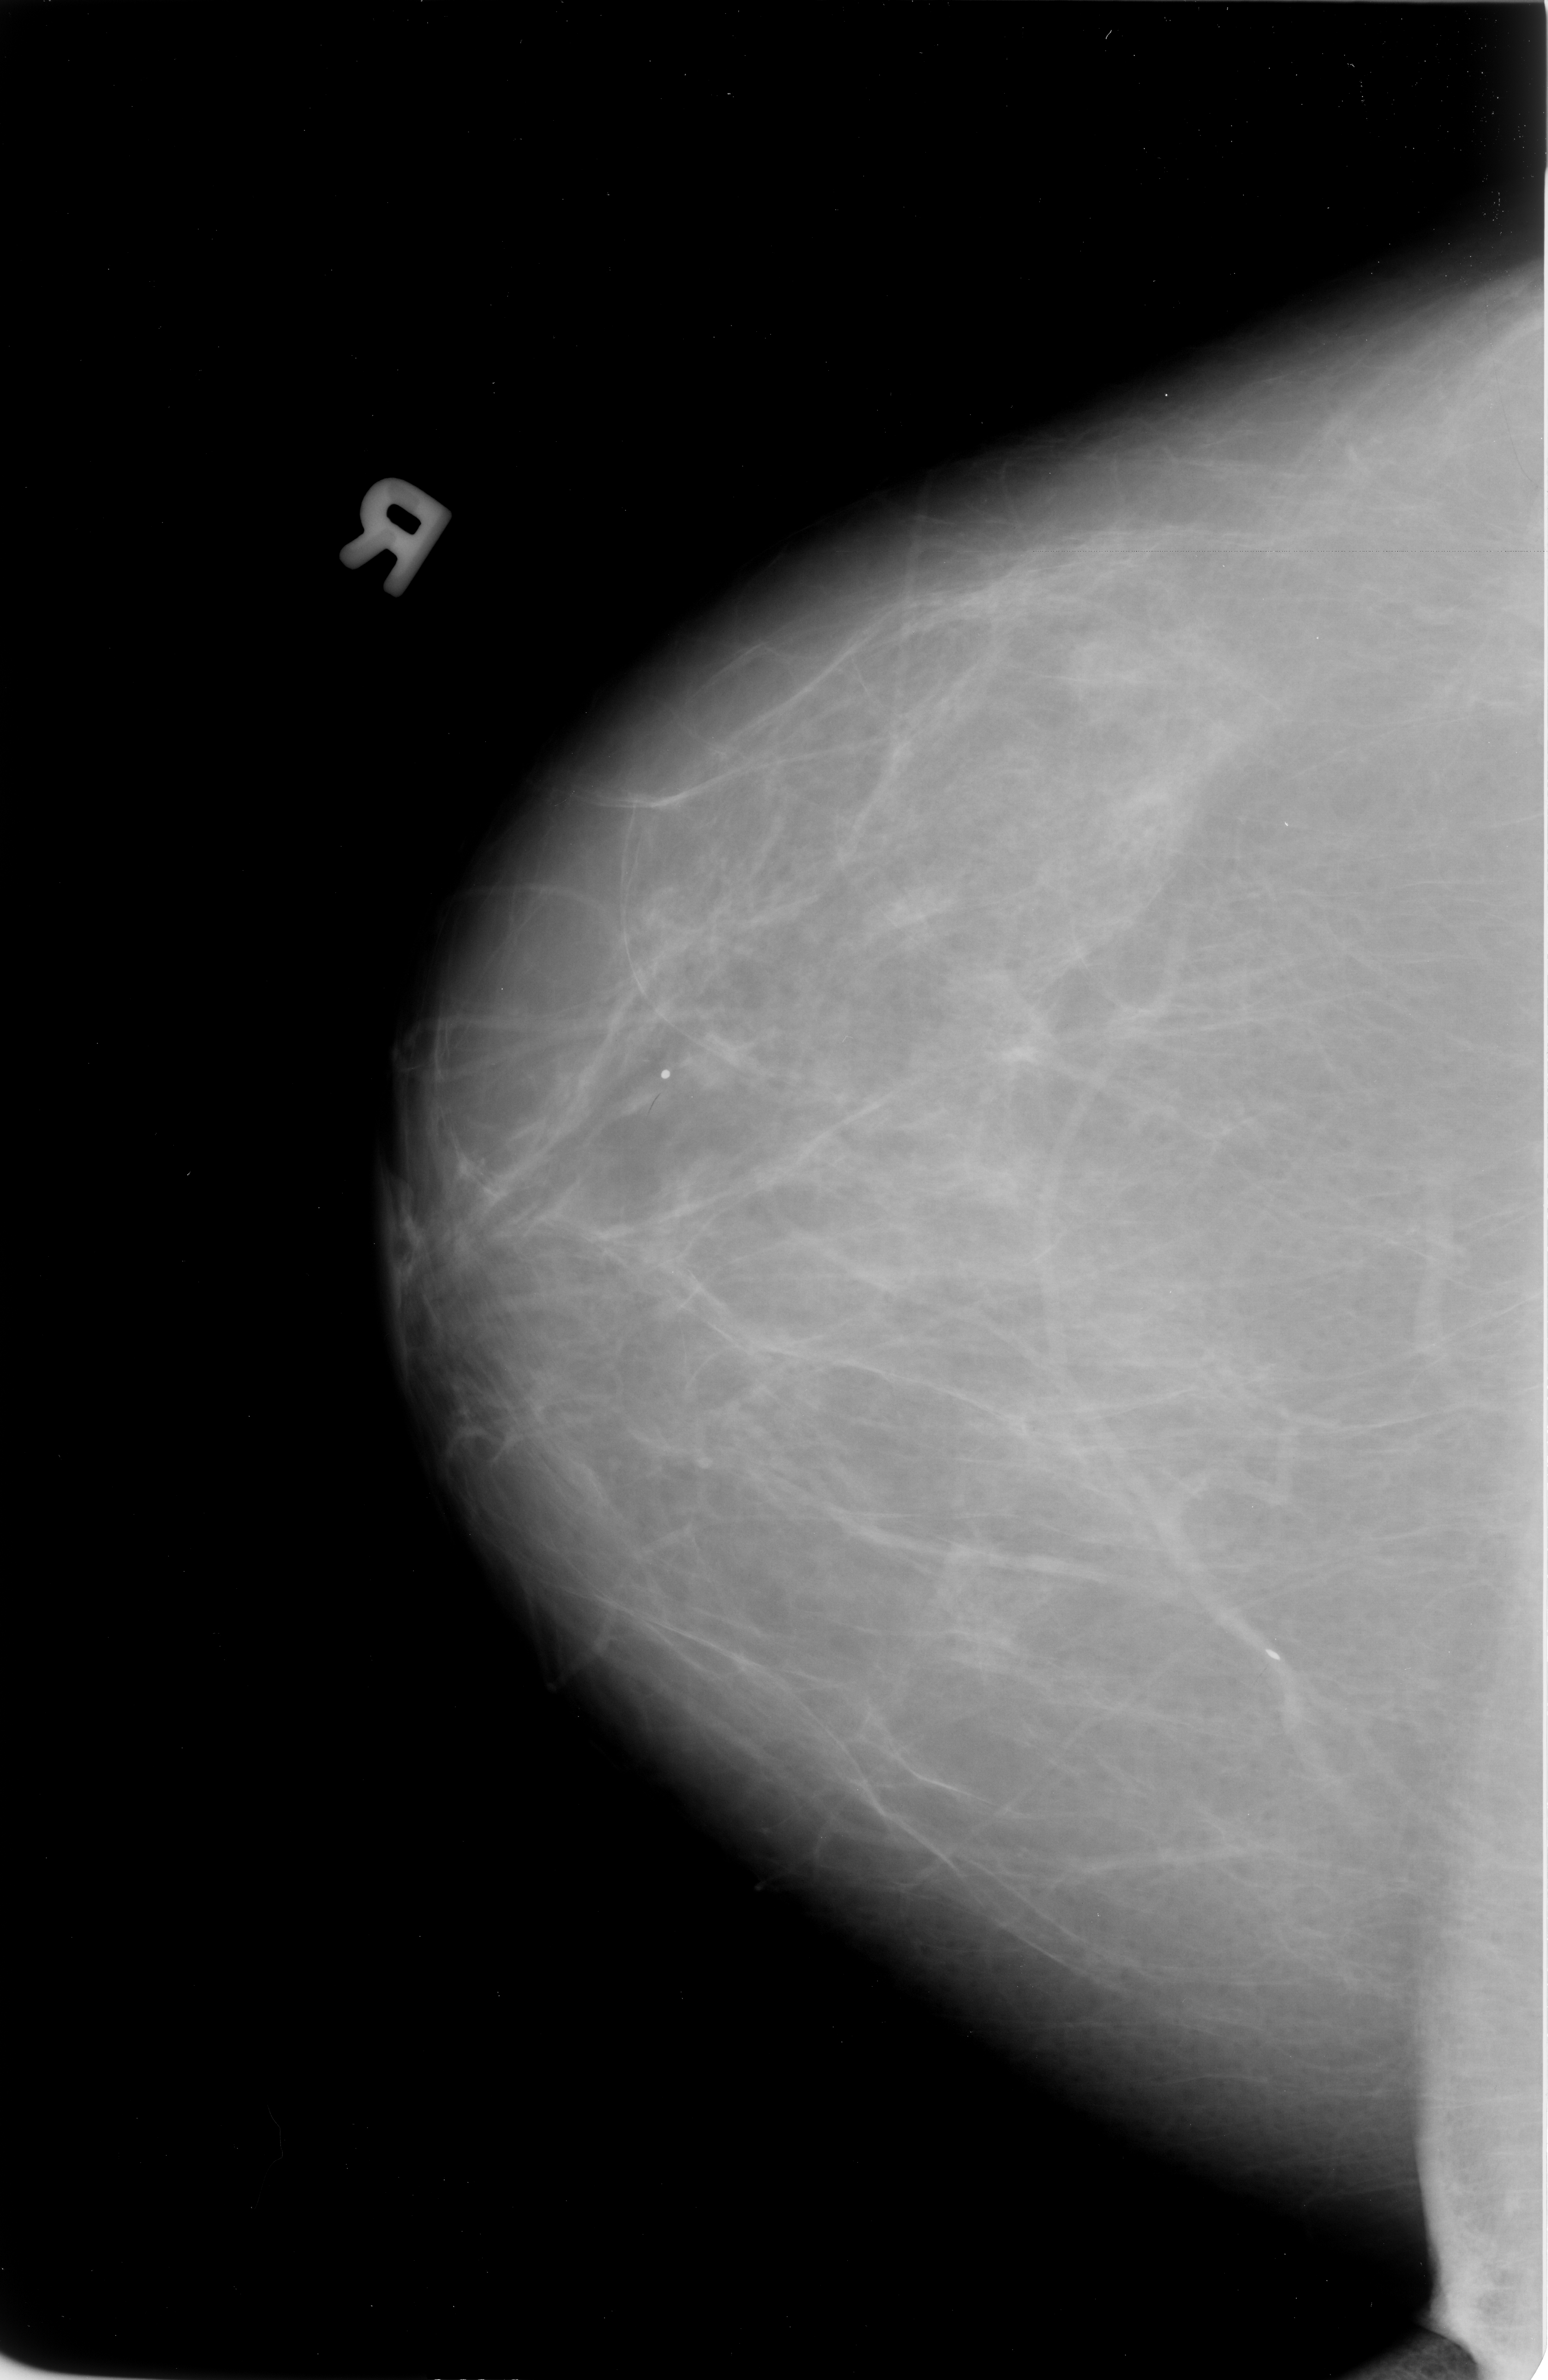
Scanned film-screen mammogram, right breast, CC view.
Radiologist-marked abnormalities on this image: Finding 1 of 2: calcifications, morphology vascular; BI-RADS assessment category 2; subtlety rating 3 on a 1 (subtle) to 5 (obvious) scale; benign; no additional work-up was recommended (benign without callback). Finding 2 of 2: calcifications, morphology coarse; BI-RADS assessment category 2; benign without callback (not worked up further).